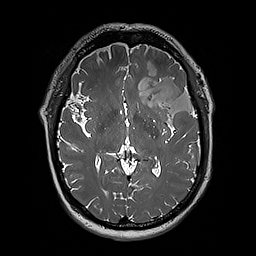
Brain MRI from a brain-tumour surgery series, one axial slice; slice 112 of 192 in the series (ordered by position); 256 × 256 image matrix. From the clinical record (not read from this slice): histopathology: Oligodendroglioma; WHO grade: 3; IDH mutation: yes.
Annotated regions visible in this slice (outlined manually by an expert reader):
- tumour: box from (x=124, y=60) to (x=197, y=125) px